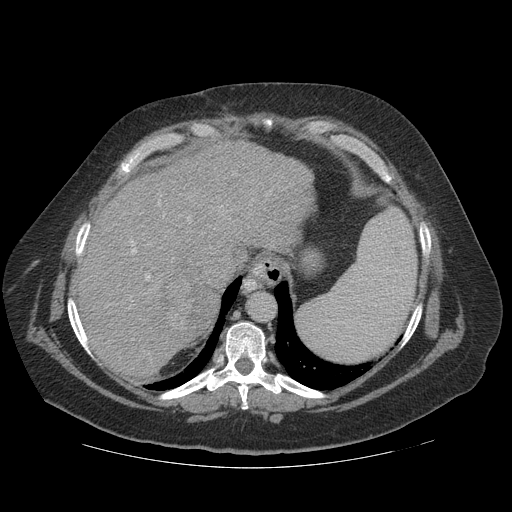
Contrast-enhanced abdominal CT (liver protocol), one axial slice; position 92 of 121 along the scan axis; 140 kVp; soft-tissue window (W 400 / L 40 HU); 2.5 mm slice thickness; 512 × 512 image matrix. Case-level facts recorded for this patient, not image findings: diagnosis: hepatocellular carcinoma (patient treated with transarterial chemoembolisation; whether this scan precedes or follows treatment is not stated here); TNM stage (as recorded): Stage-IIIA; Child-Pugh class: A; tumour differentiation: well differentiated.
Outlined on this slice (semi-automatically segmented with operator editing):
- abdominal aorta: bounding box <250,293,275,322> (left, top, right, bottom; pixels)
- liver parenchyma outside the tumour (the mass and vessels are separate outlines, so this box may not span the whole liver): <72,142,312,378>
- mass: <161,264,218,349>
- liver vessels: <130,200,223,340>